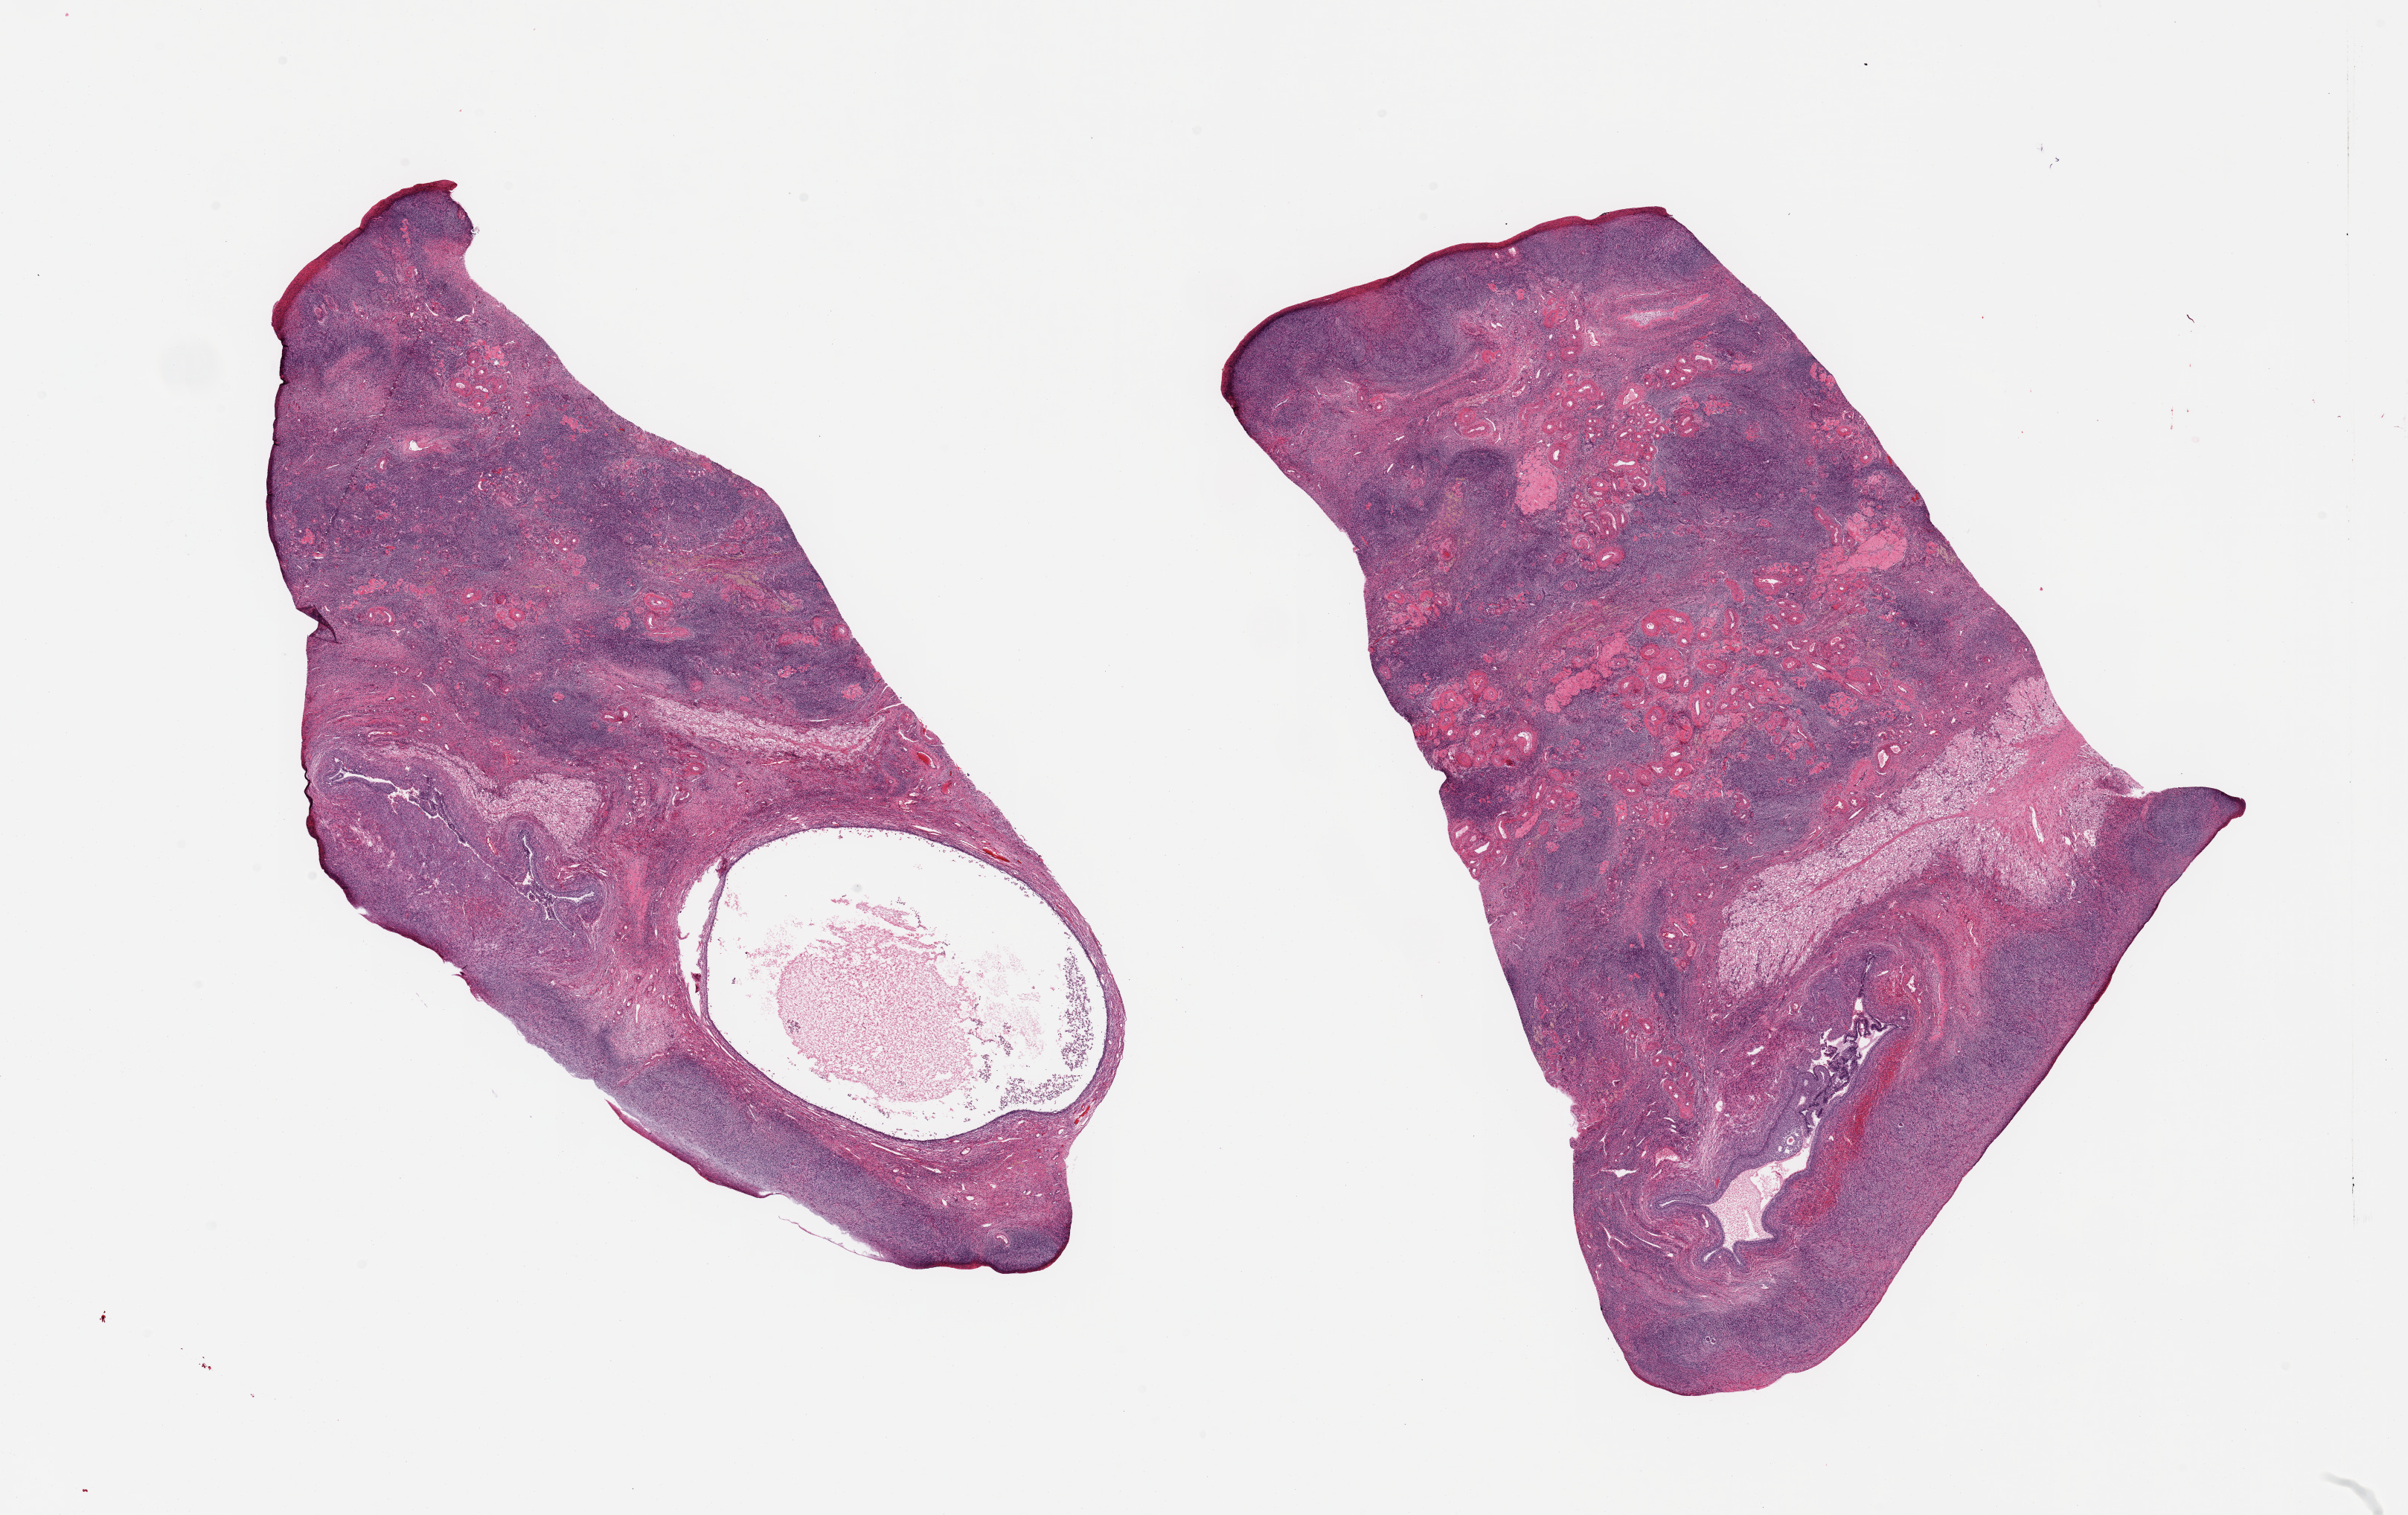
Hematoxylin and eosin (H&E) whole-slide image, low-resolution overview of the scanned area, about 25.6 x 16.1 mm, PAXgene-fixed paraffin-embedded (PFPE) section, sampled site (target tissue): ovary, tissue donor sample. Female donor.
• reviewer comment on this tissue sample: 2 pieces; variety of cysts: follicular, corpus luteum, albicans